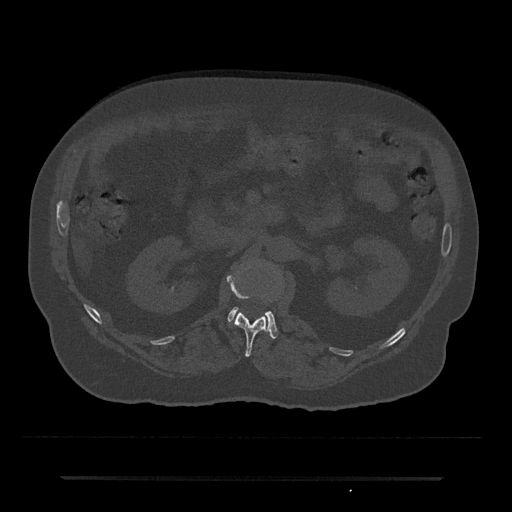
CT including the spine, one axial slice; slice 47 of 797 in the series (ordered by position); 120 kVp; bone window (W 1800 / L 400 HU); 512 × 512 image matrix, field of view 437 × 437 mm. Patient: male, 69 years. Case-level facts recorded for this patient, not image findings: primary cancer: prostate.
Outlined on this slice (semi-automatically segmented with operator editing):
- L1 vertebra: bounding box [x1, y1, x2, y2] px = [226, 271, 267, 357]
- L2 vertebra: [228, 307, 278, 339]